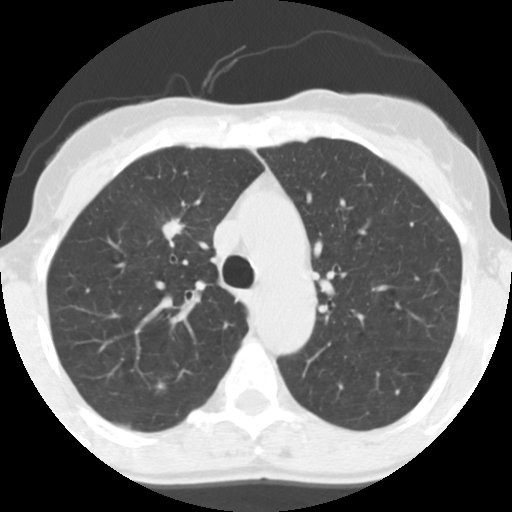
Axial slice from a low-dose chest CT screening exam; baseline annual screen; lung window (W 1500 / L -600 HU); standard (soft-tissue) reconstruction kernel (STANDARD); 512 × 512 image matrix. Female participant, aged 56 years at enrolment. Former smoker at enrolment.
Lesion marked by an expert reader, bounding box [x1, y1, x2, y2] px = [151, 210, 192, 249]. Reader record for this screening exam (exam-level; its link to the box is not recorded): non-calcified nodule or mass ≥4 mm, right upper lobe, 12 × 9 mm, spiculated (stellate) margins, soft tissue attenuation. Official screen result: positive, change unspecified: nodule(s) >= 4 mm or enlarging nodule(s), mass(es), or other non-specific abnormalities suspicious for lung cancer. Later outcome: lung cancer diagnosed 779 days after this screen (after the third annual screen) — adenocarcinoma, NOS, right upper lobe, moderately differentiated (G2), stage IA (AJCC 6th edition), 19 mm at pathology.